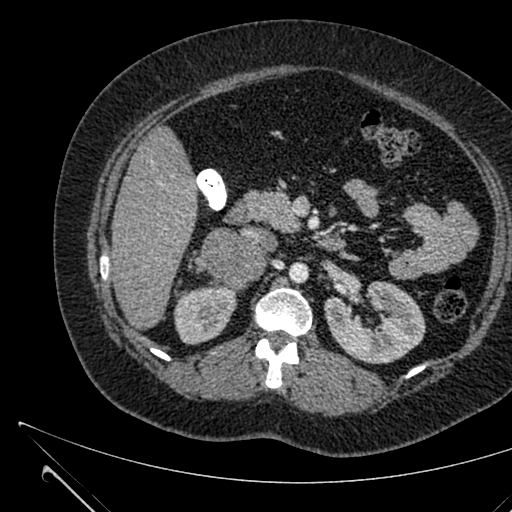
Contrast-enhanced abdominal CT, one axial slice. Position 366 of 731 along the scan axis. 120 kVp. Intravenous contrast given. Soft-tissue window (W 400 / L 40 HU). 512 × 512 image matrix, field of view 376 × 376 mm. Patient: female, 36 years. From the clinical record (not read from this slice): diagnosis: adrenocortical carcinoma; tumour side: right adrenal; tumour size at pathology: 10 cm; Ki-67 index: 20 %; stage (as recorded): 4.
Structures marked on this image (semi-automatically segmented with operator editing):
- mass: bounding box <201,228,266,288> (left, top, right, bottom; pixels)